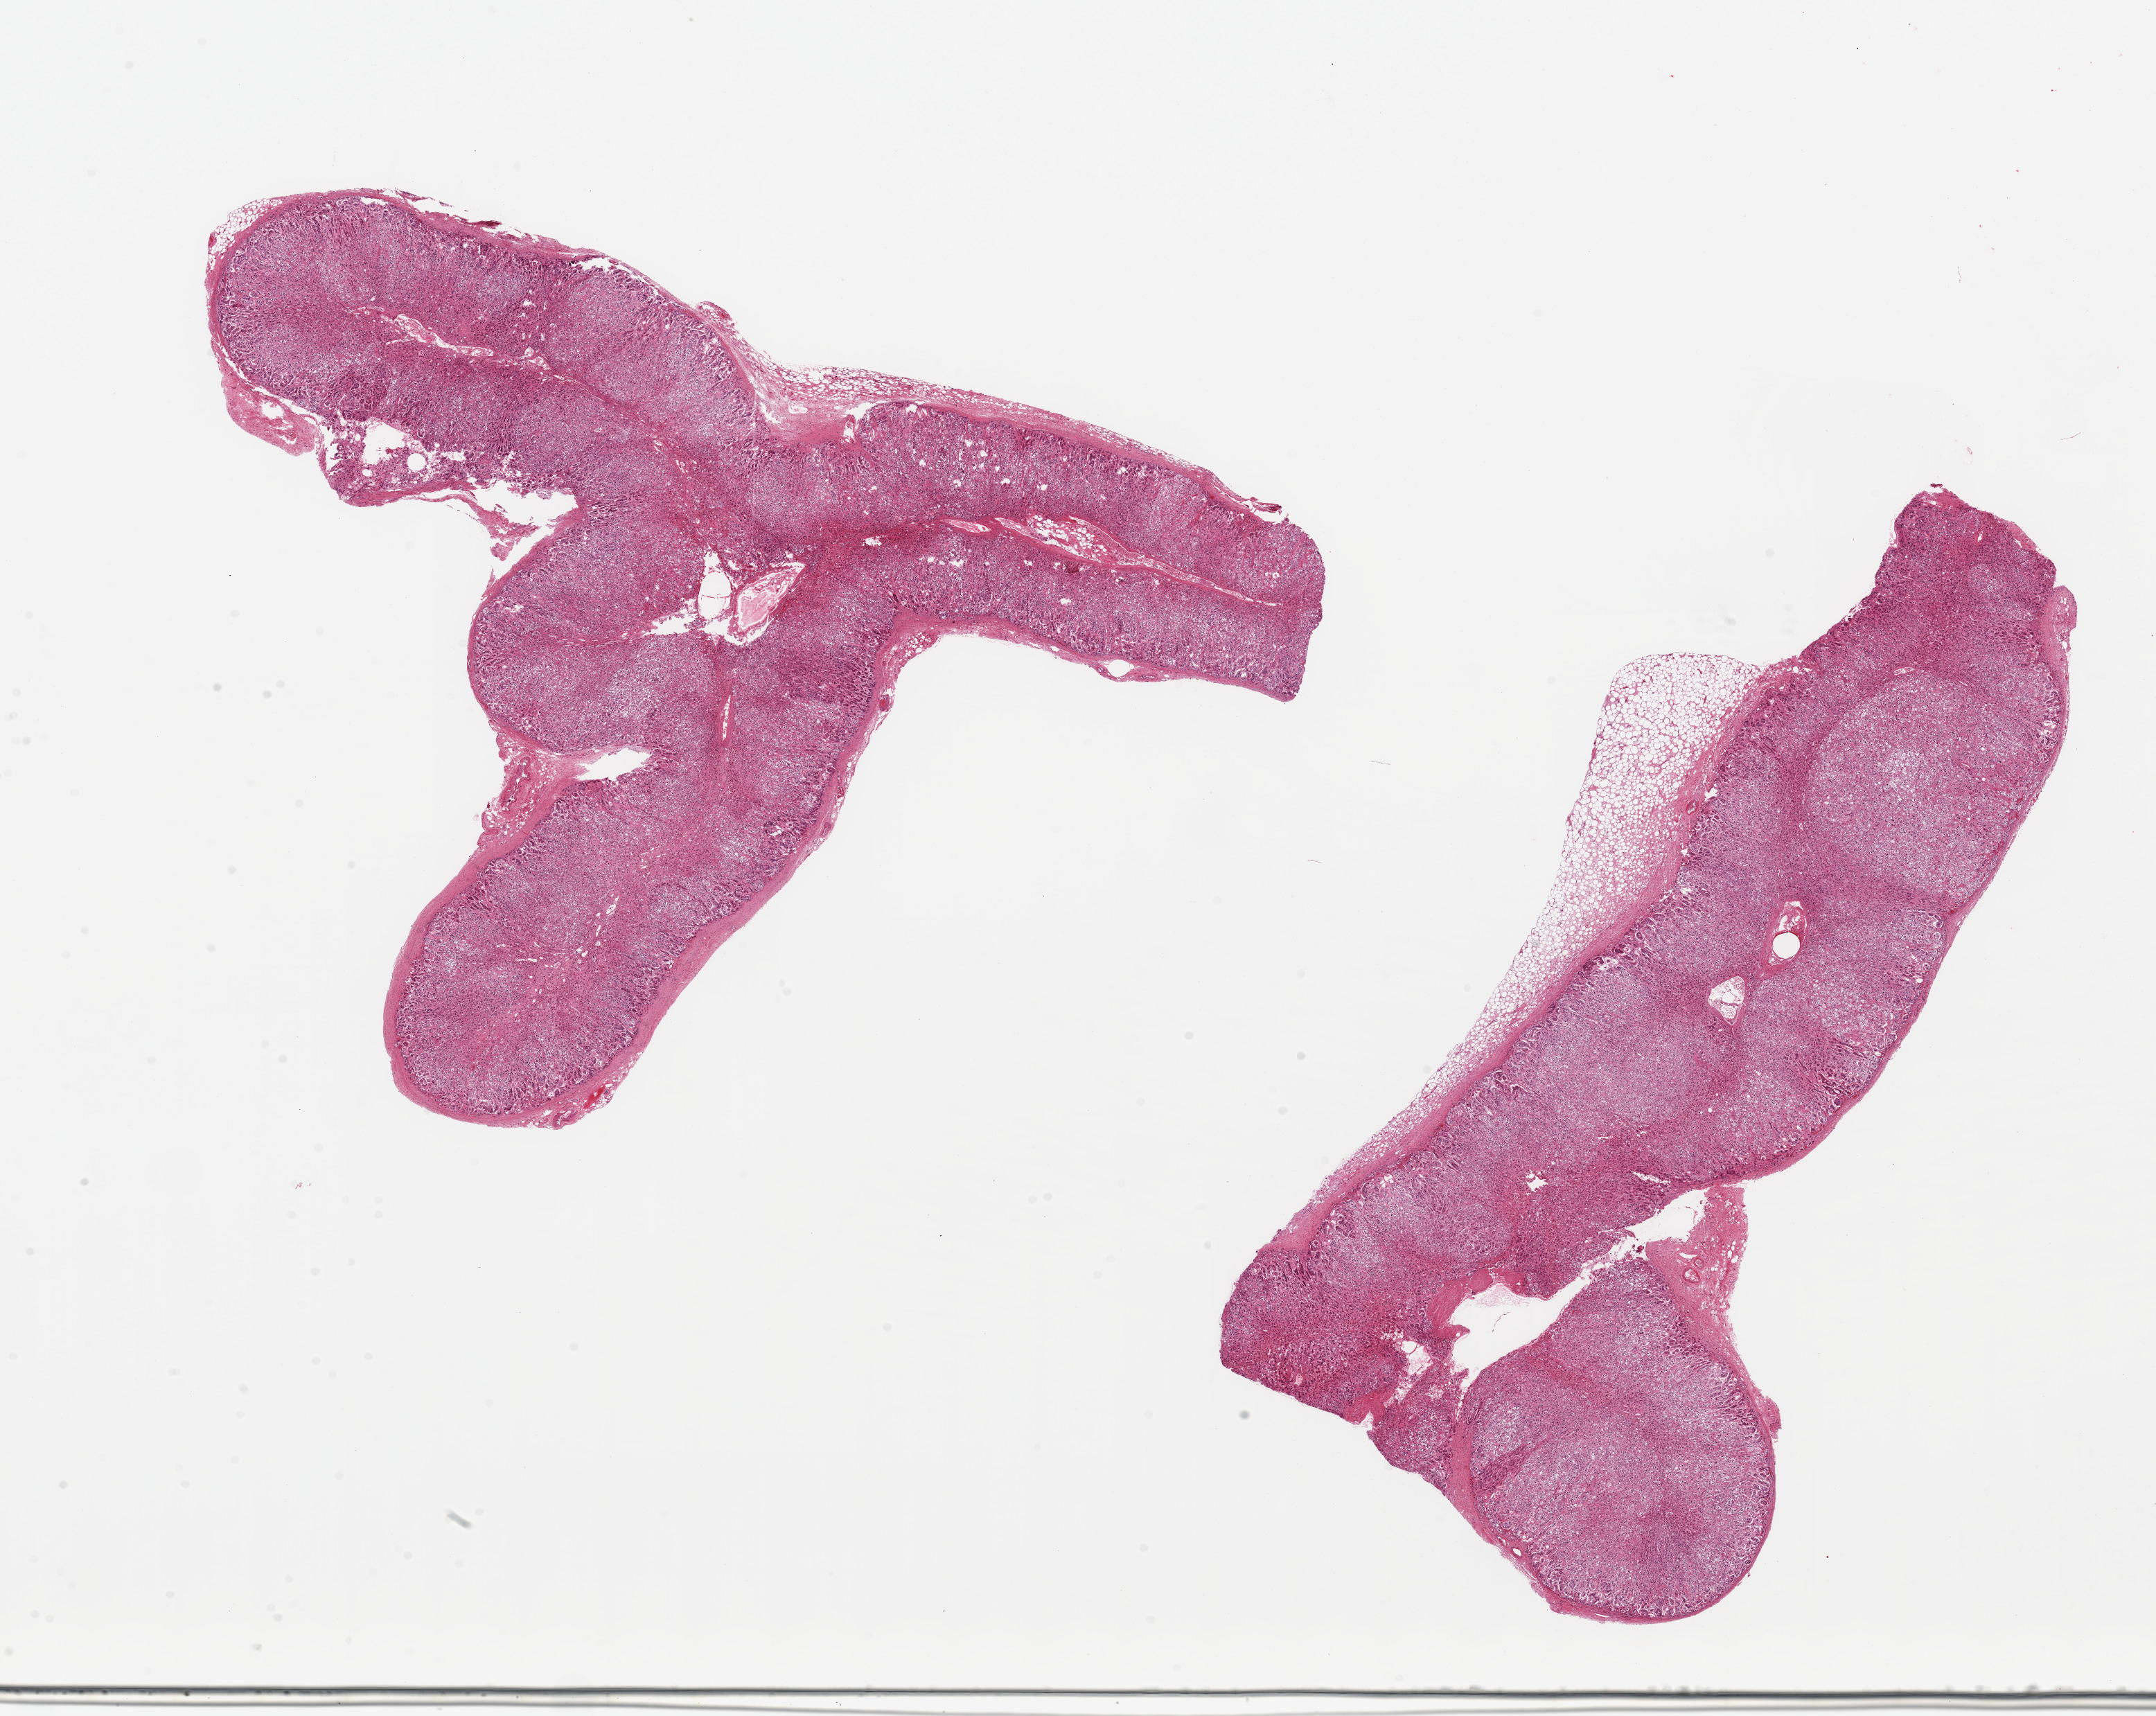
Digitized H&E-stained section, low-resolution overview of the scanned area, about 24.6 x 19.6 mm (slide scanned at 20x); PAXgene-fixed paraffin-embedded (PFPE) section; section of adrenal gland (target tissue); donor tissue sample. Donor sex: male.
Reviewer comment on this tissue sample: 2 ~10x8mm pieces, all cortex.